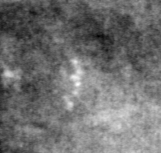
Crop from a digitized film mammogram around one marked abnormality, right breast, CC view, BI-RADS breast density category 2 (scale 1–4).
Finding: calcifications, morphology pleomorphic, distribution clustered; BI-RADS assessment category 4; pathology result (as recorded, not read from the image): benign.